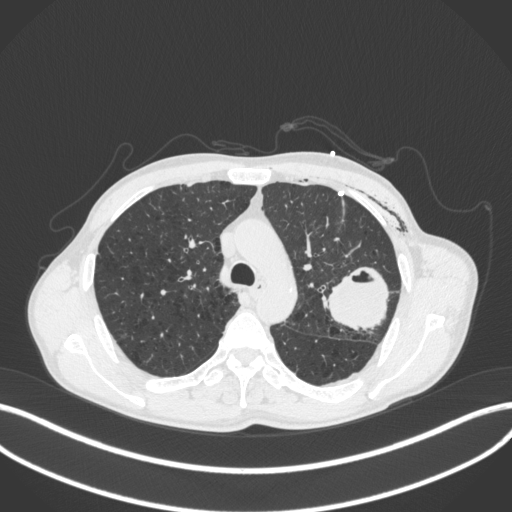
Chest CT, one axial slice; position 283 of 416 along the scan axis; reconstruction kernel B31f; 120 kVp; lung window (W 1500 / L -600 HU); 1 mm slice thickness; 512 × 512 image matrix, field of view 400 × 400 mm. Patient: male, 58 years. Case-level facts recorded for this patient, not image findings: clinical TNM (as recorded): T3 N0 M0.
Annotated regions visible in this slice (rectangle marked by the reading radiologist):
- lung tumour (recorded histology: adenocarcinoma): bounding box <326,263,392,332> (left, top, right, bottom; pixels)